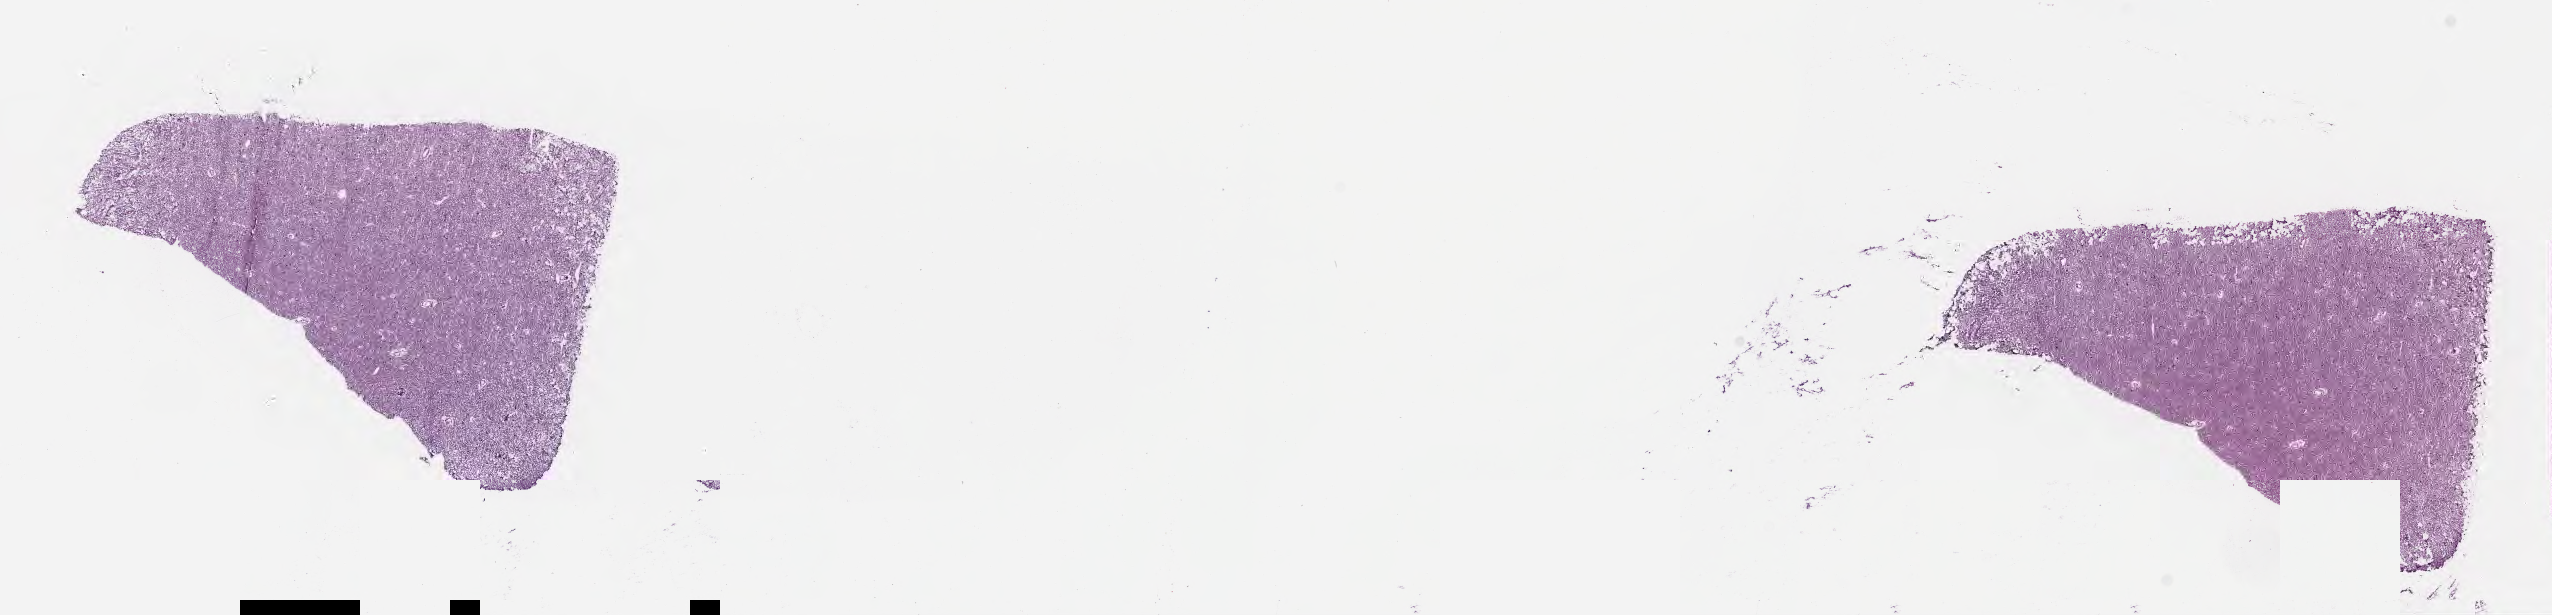
Hematoxylin and eosin (H&E) whole-slide image, low-resolution overview of the scanned area, about 20.6 x 5.0 mm; cryosection; primary tumor; anatomic site: spleen. Patient female; aged 15. Composition of this section per pathologist review: tumor cells 5%, tumor nuclei 30%, stromal cells 5%, necrosis 90%, normal cells 0%. Infiltration values recorded for this section: lymphocyte infiltration 5%, monocyte infiltration 5%, neutrophil infiltration 0%.
Diagnosis: Burkitt lymphoma, NOS. Section: top of the tissue portion. Ann Arbor stage (patient): Stage III.